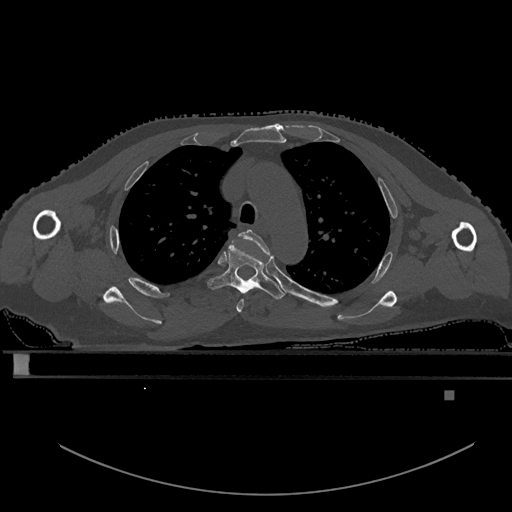
CT including the spine, one axial slice; position 417 of 969 along the scan axis; bone window (W 1800 / L 400 HU); 0.5 mm slice thickness; 512 × 512 image matrix, field of view 456 × 456 mm. Patient: male, 82 years. Case-level facts recorded for this patient, not image findings: primary cancer: prostate; vertebrae with lytic lesions (as recorded): T11, T9, T8, T2.
Outlined on this slice (semi-automatically segmented with operator editing):
- T3 vertebra: bounding box (x1, y1, x2, y2) in pixels: (236, 229, 270, 313)
- T4 vertebra: (207, 244, 285, 300)